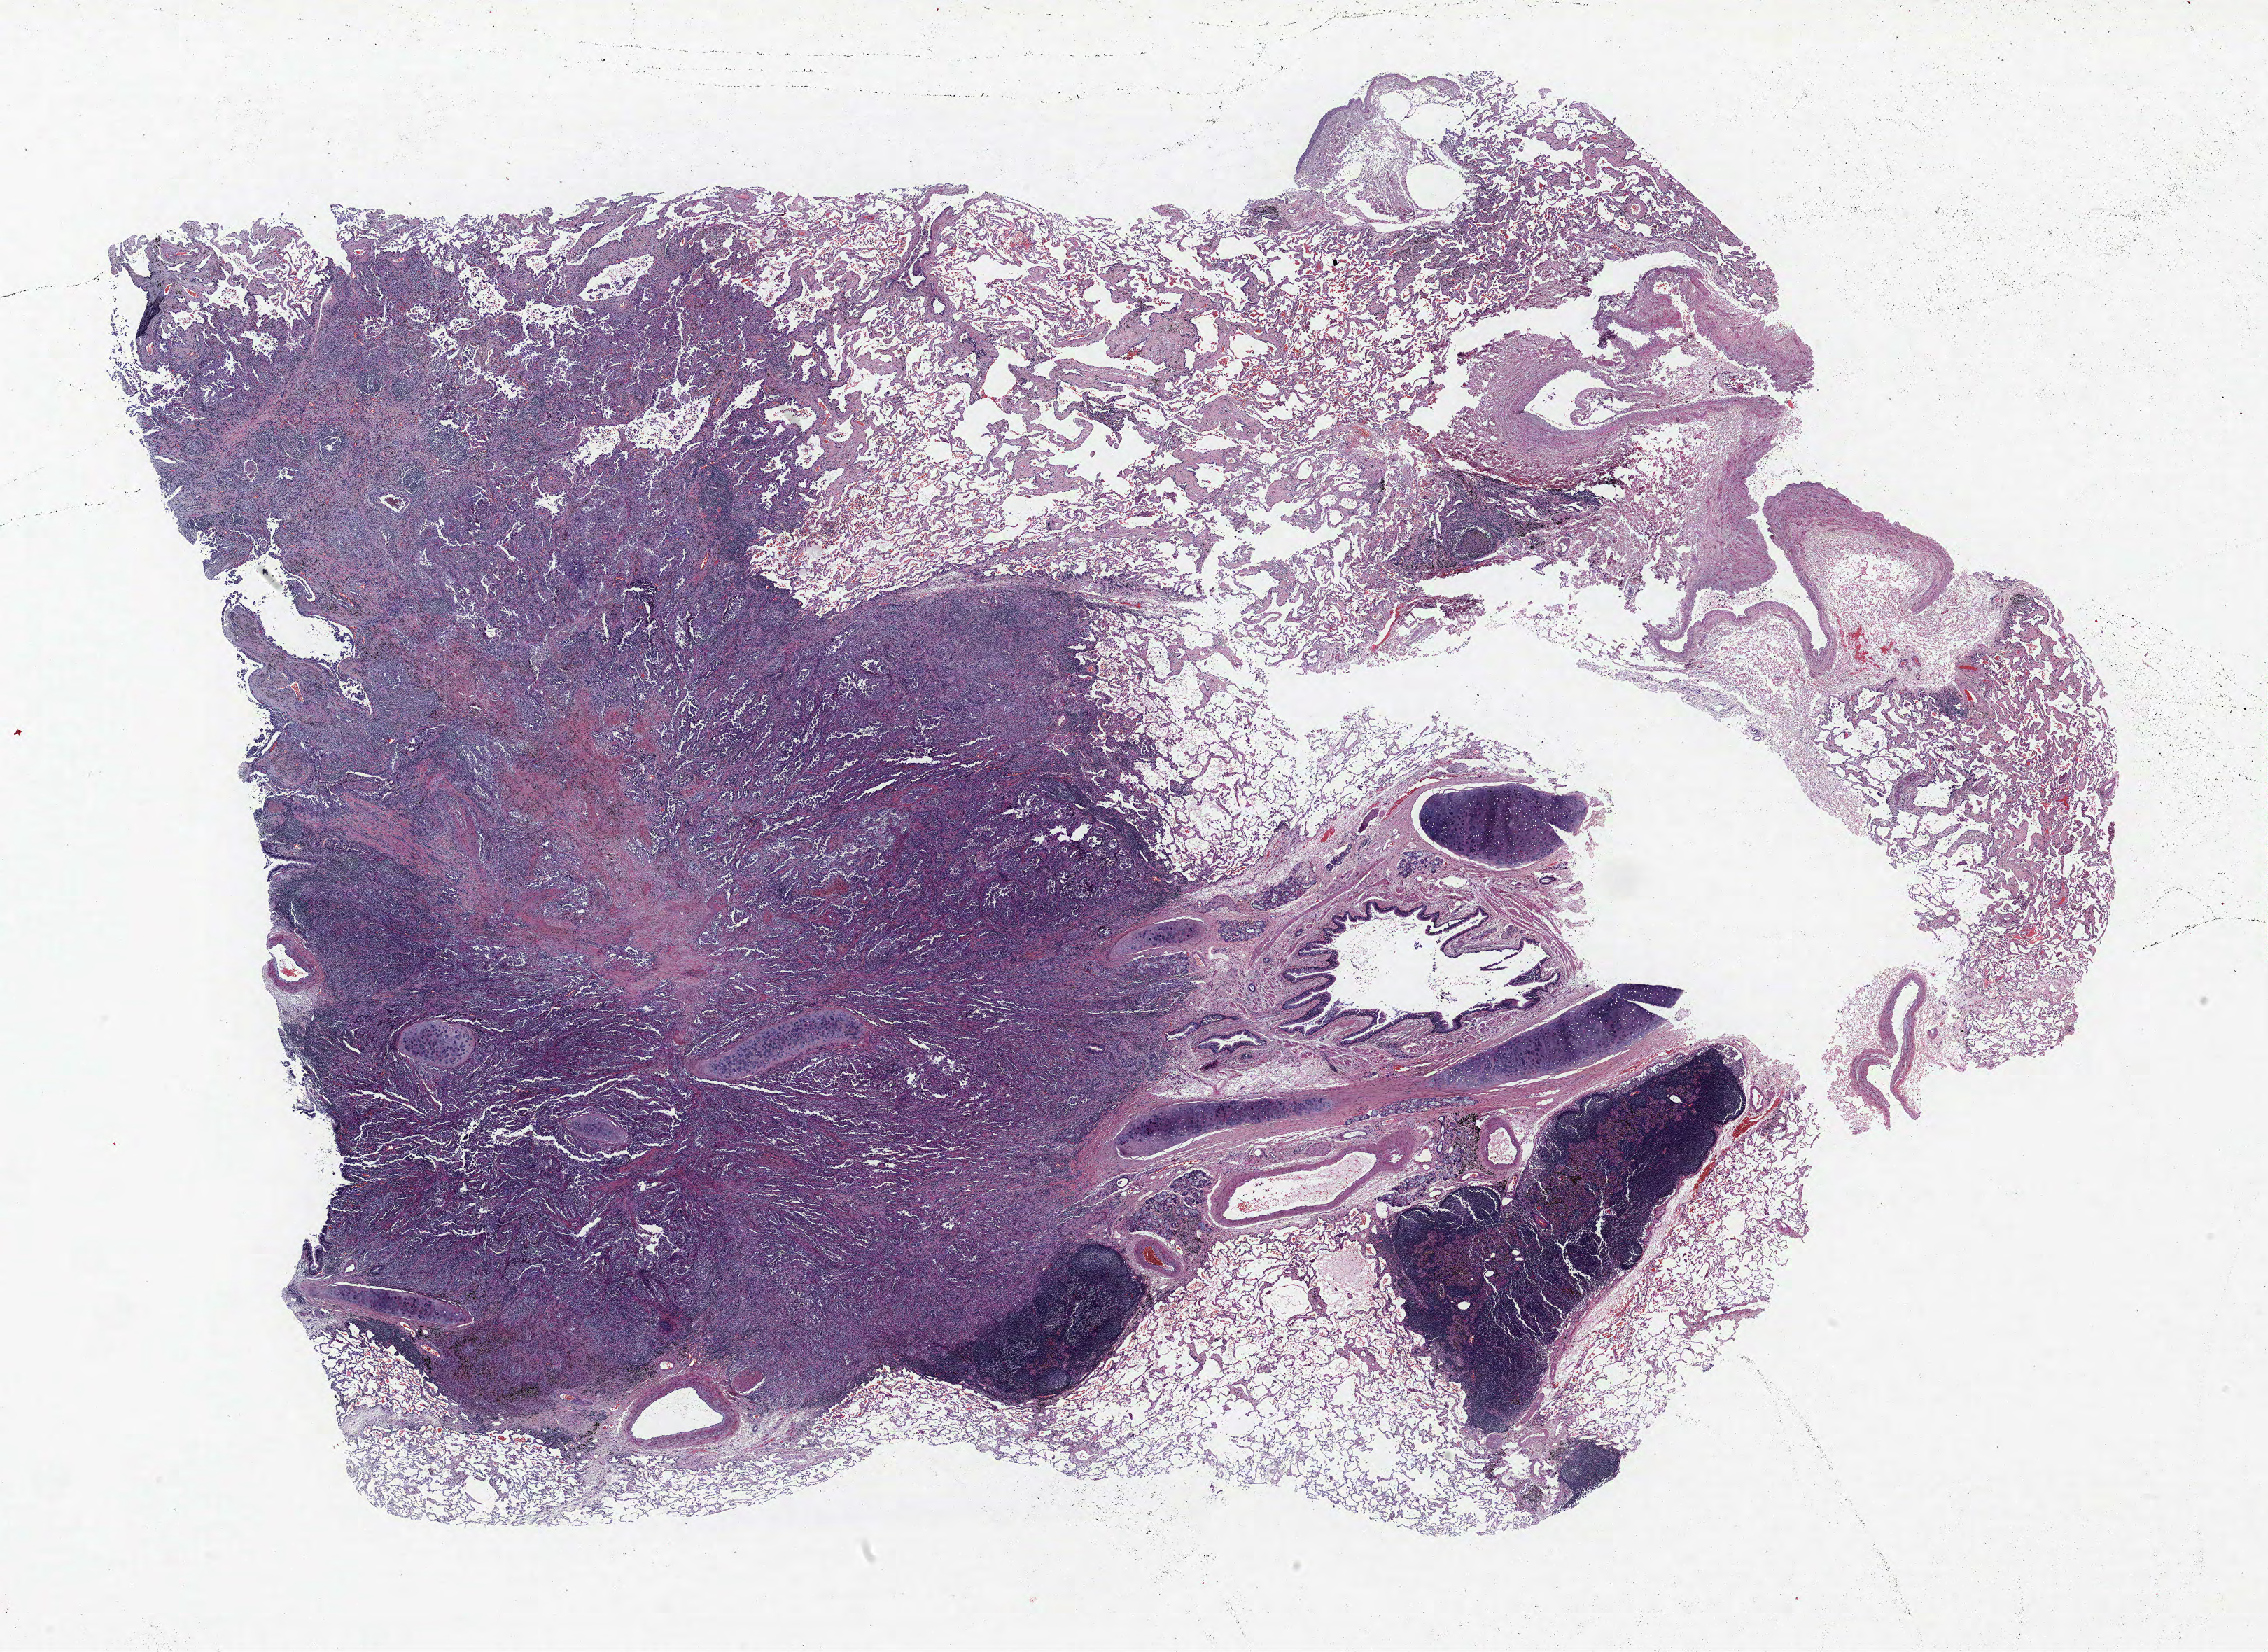
Whole-slide histology image, H&E, whole scanned area (about 25.9 x 18.9 mm, slide scanned at 40x) shown as a low-resolution overview; FFPE section; lung tissue. Female patient, aged 66 at enrolment. Grade: poorly differentiated (G3).
* participant's lung-cancer diagnosis: Adenocarcinoma, NOS (ICD-O-3 8140/3)
* tumour size (pathology): 18 mm
* primary tumour location (clinical record): right upper lobe
* stage (AJCC 6th edition): IA
* ICD-O-3 topography: upper lobe of lung (C34.1)